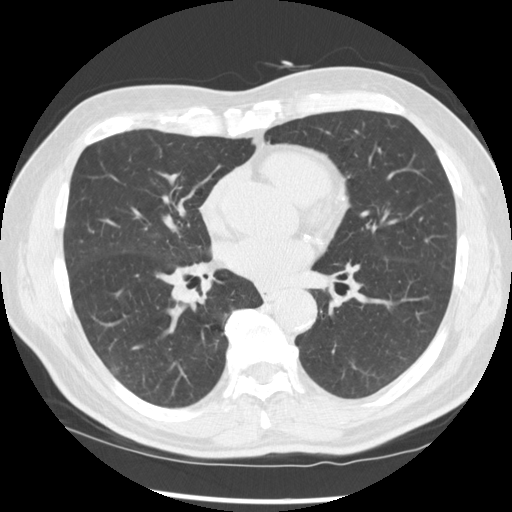
Low-dose screening chest CT, one axial slice. Reconstruction kernel STANDARD. 120 kVp. Lung window (W 1500 / L -600 HU). 2.5 mm slice thickness. 512 × 512 image matrix, field of view 365 × 365 mm.
Structures marked on this image (outlined manually by an expert reader):
- lesion 1 (tumor, middle lobe of right lung): box from (x=171, y=279) to (x=202, y=307) px